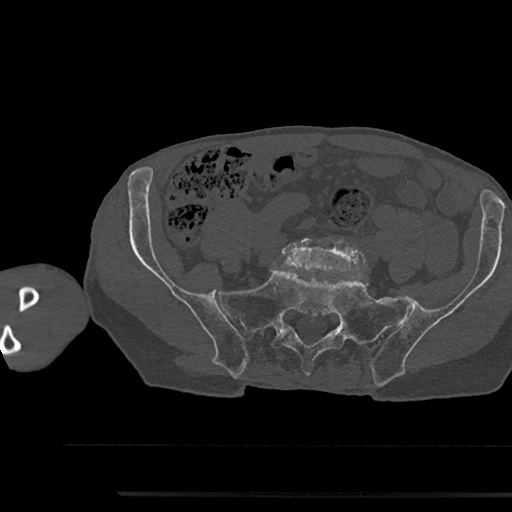
CT including the spine, one axial slice. Slice 297 of 797 in the series (ordered by position). Reconstruction kernel Br40s/3. Bone window (W 1800 / L 400 HU). 0.5 mm slice thickness. 512 × 512 image matrix, field of view 367 × 367 mm. Male patient, age 79 years. From the clinical record (not read from this slice): primary cancer: prostate.
Structures marked on this image (semi-automatic segmentation, software-assisted and operator-edited):
- L5 vertebra: bounding box (x1, y1, x2, y2) in pixels: (281, 237, 367, 273)